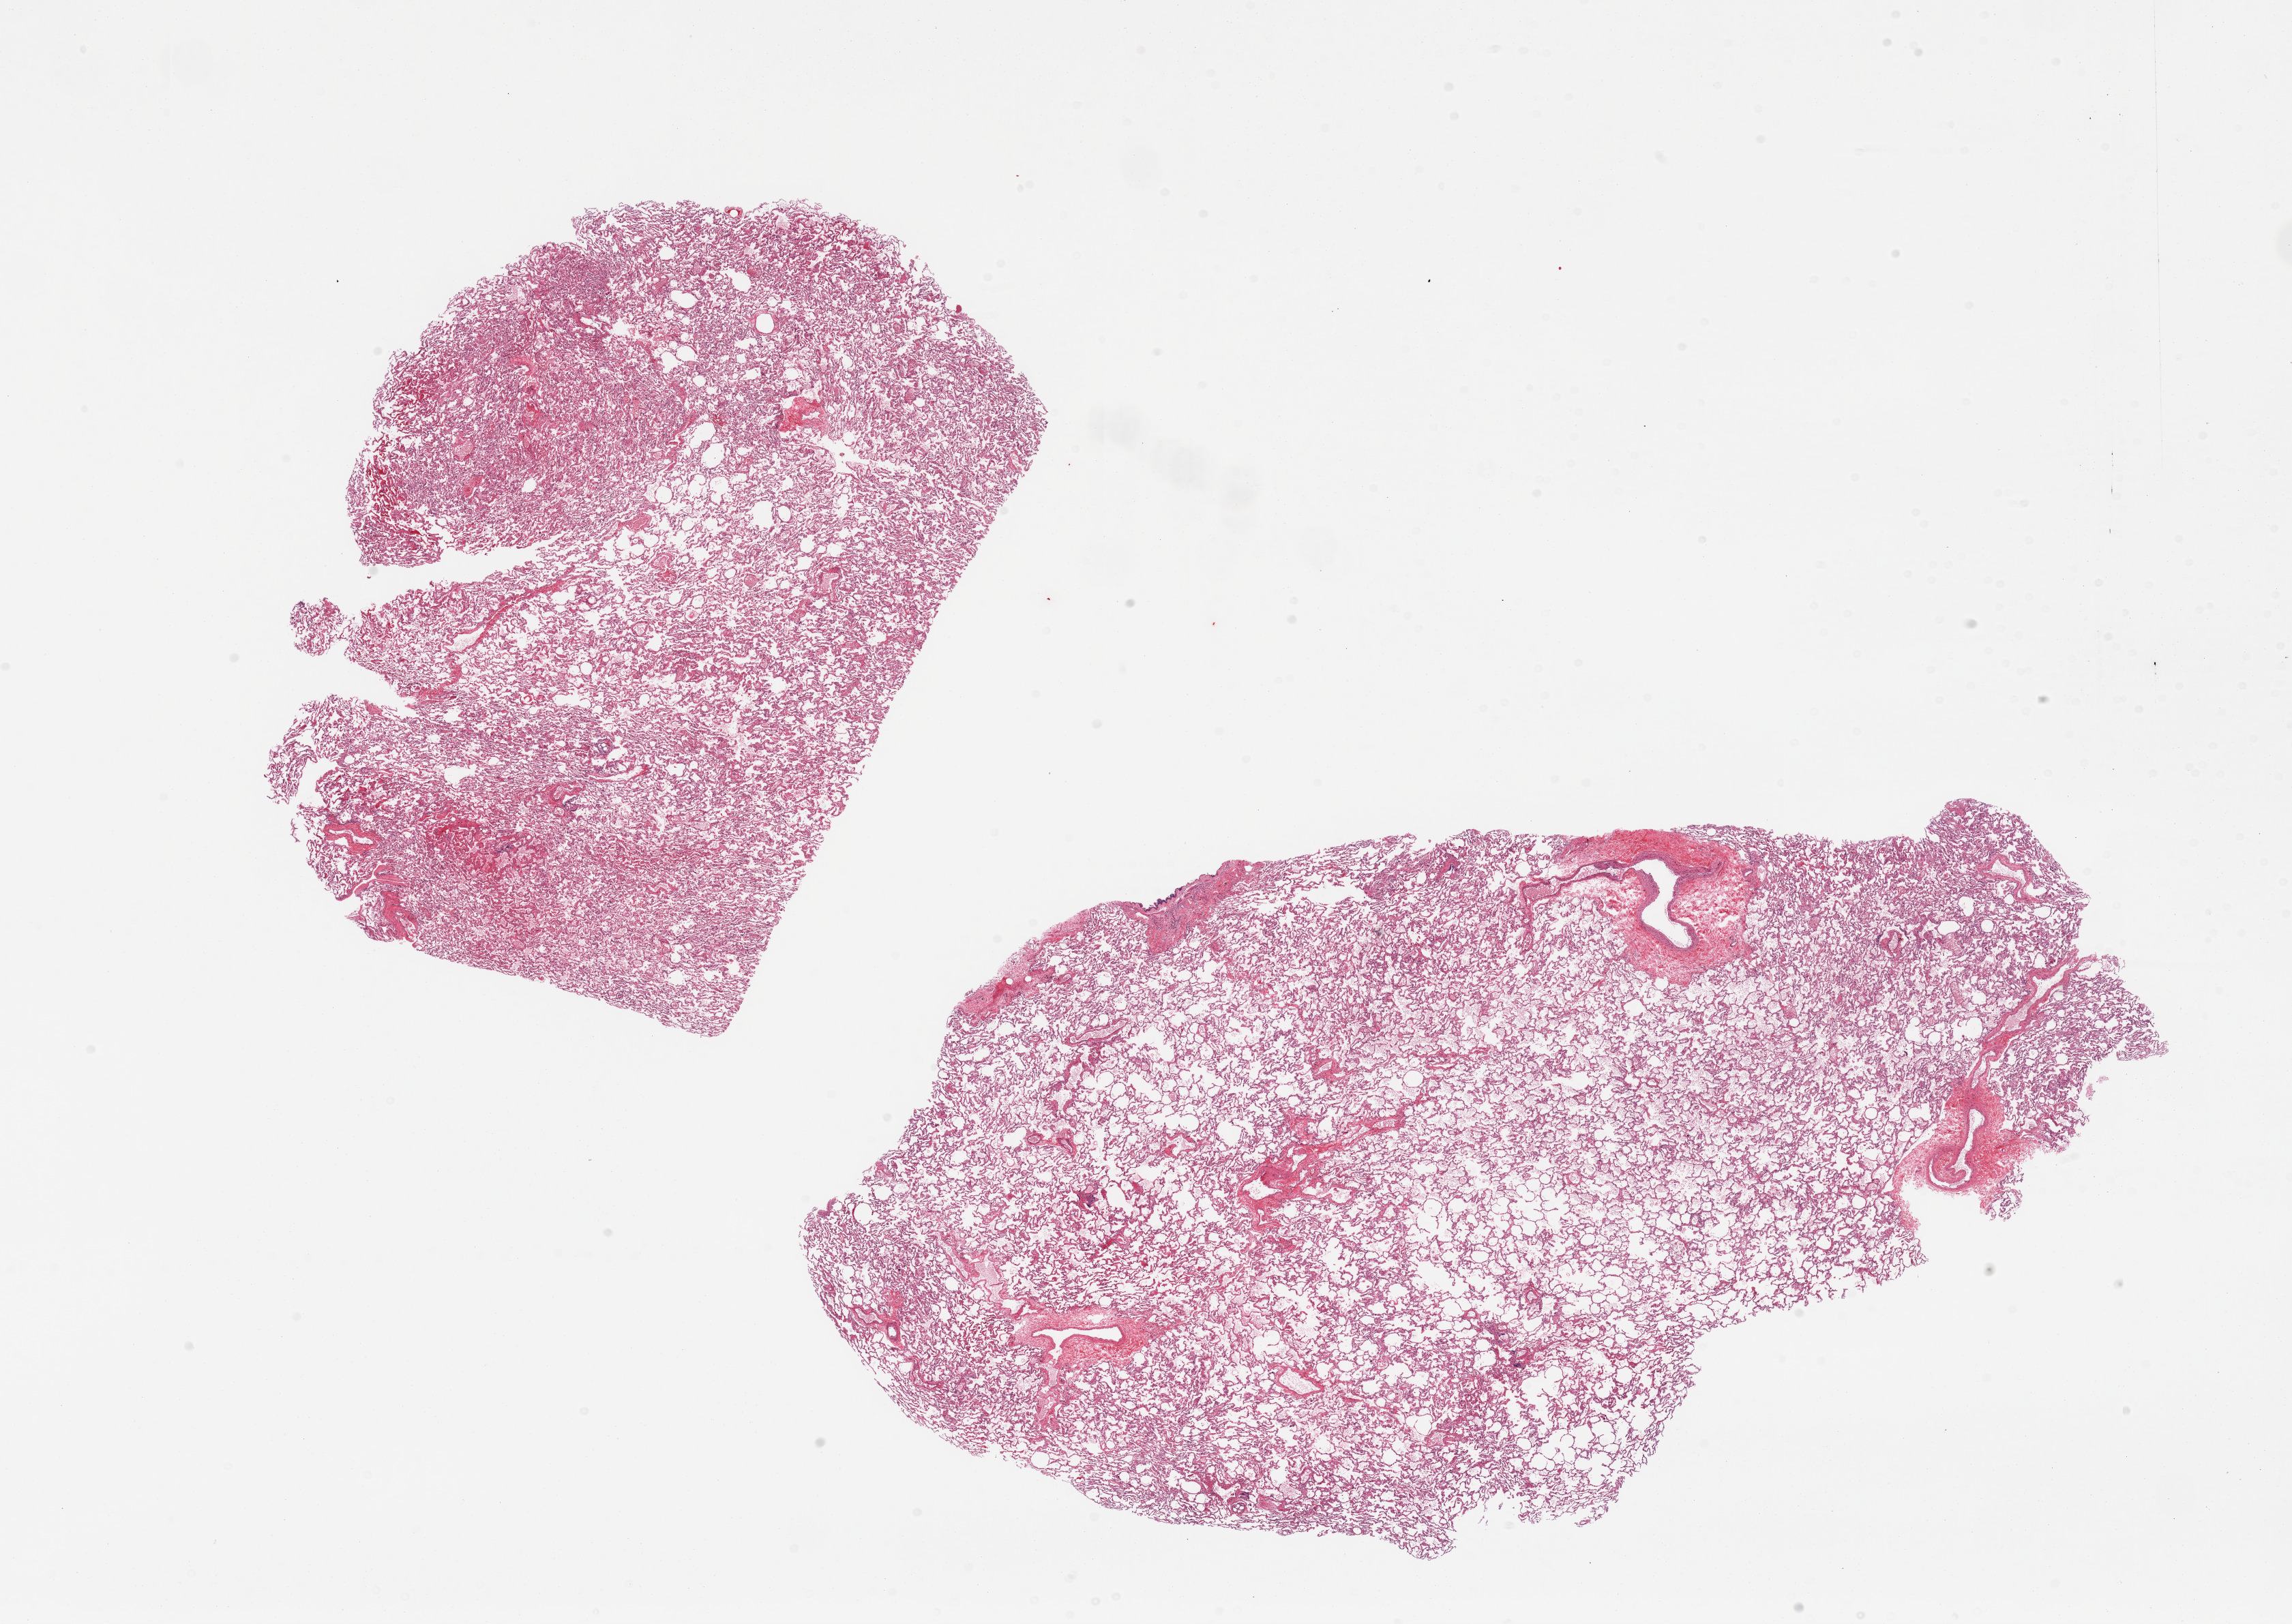
Whole-slide image, H&E stain, brightfield, a low-resolution overview of the entire scanned area, about 26.6 x 18.8 mm. PAXgene-fixed, paraffin-embedded tissue. Target tissue: lung. Tissue donor sample. Donor sex: female.
Pathologist's review note for this sample: 2 pieces.